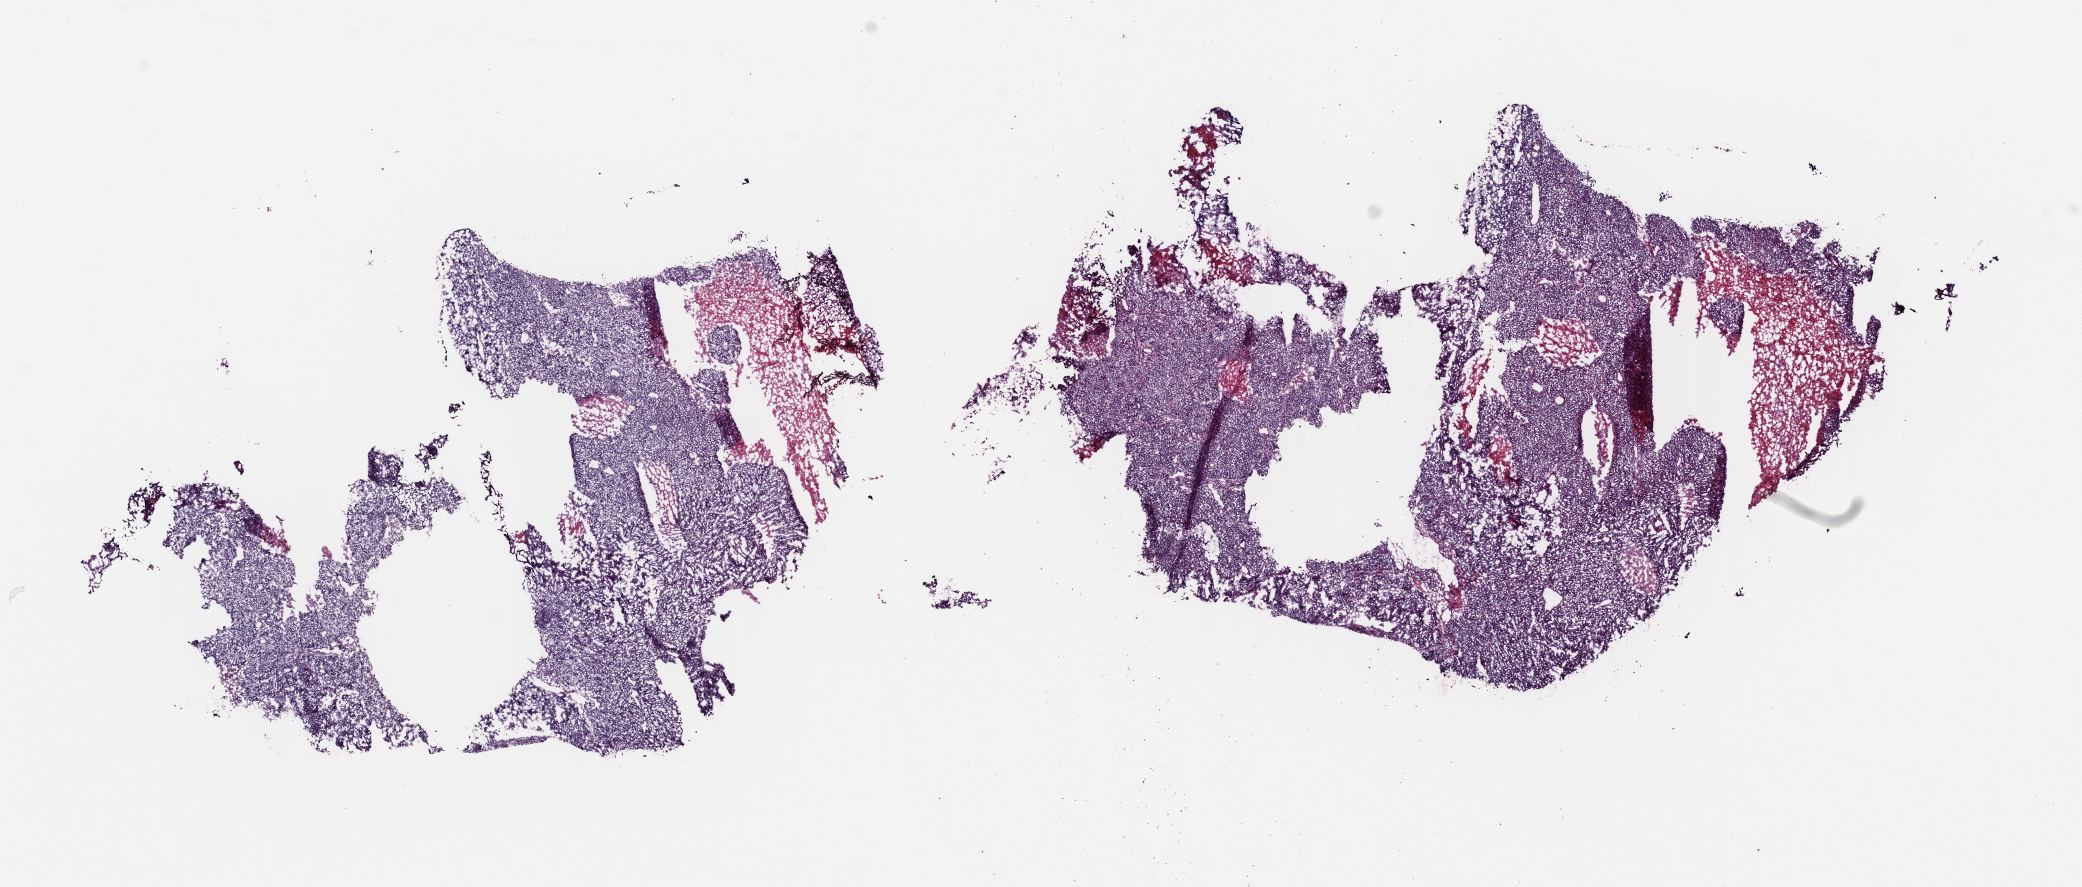
H&E whole-slide image — low-resolution overview of the scanned area, about 16.4 x 7.0 mm (from a 40x scan), frozen section from the top of the tissue portion, primary tumour sample from the uterus. Patient: female, age at initial diagnosis 49 years. Histologic grade: G3 (poorly differentiated). Composition of this section per pathologist review: tumour cells 80%, tumour nuclei 80%, normal cells 0%, stromal cells 10%, necrosis 10%. Inflammatory infiltration, as recorded: lymphocyte infiltration 40%, monocyte infiltration 20%, neutrophil infiltration 20%.
• histologic diagnosis: Endometrioid adenocarcinoma, NOS (endometrium)
• FIGO stage: IA